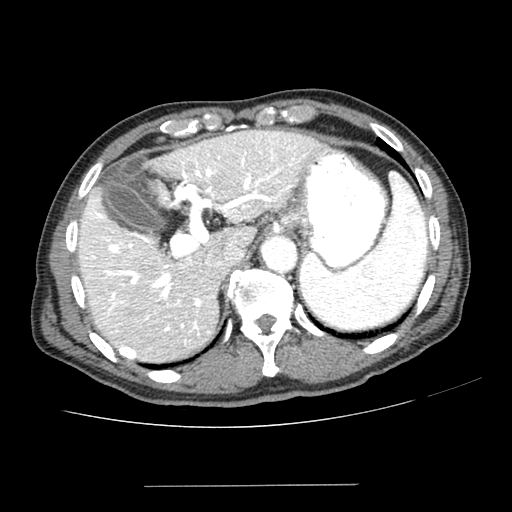
Contrast-enhanced abdominal CT (liver protocol), one axial slice. Slice 164 of 187 in the series (ordered by position). Reconstruction kernel SOFT. 100 kVp. One of 2 acquisitions stored at this slice position. Soft-tissue window (W 400 / L 40 HU). 512 × 512 image matrix. From the clinical record (not read from this slice): diagnosis: hepatocellular carcinoma (patient treated with transarterial chemoembolisation; whether this scan precedes or follows treatment is not stated here); TNM stage (as recorded): Stage-I; Child-Pugh class: A; tumour differentiation: poorly differentiated; tumour size: 1.6 cm.
Structures marked on this image (semi-automatically segmented with operator editing):
- liver parenchyma outside the tumour (the mass and vessels are separate outlines, so this box may not span the whole liver): bounding box (x1, y1, x2, y2) in pixels: (78, 132, 322, 362)
- liver vessels: (85, 146, 305, 354)